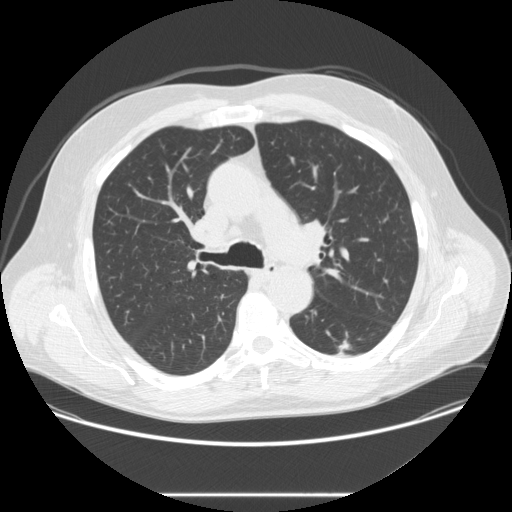
Low-dose screening chest CT, one axial slice; slice 170 of 262 in the series (ordered by position); reconstruction kernel STANDARD; lung window (W 1500 / L -600 HU); 2.5 mm slice thickness; 512 × 512 image matrix.
Structures marked on this image (outlined manually by an expert reader):
- lesion 1 (tumor, lower lobe of left lung): bounding box <337,340,351,355> (left, top, right, bottom; pixels)